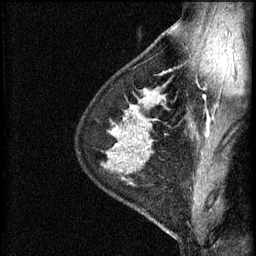
Breast MRI (dynamic contrast-enhanced), one sagittal slice. Slice 44 of 60 in the series (ordered by position). 3 images stored at this slice position (order not interpretable as contrast timing). 1.5 T. TE 4.2 ms, TR 11 ms. 2 mm slice thickness. 256 × 256 image matrix. Female patient, age 29 years.
Outlined on this slice (semi-automatically segmented with operator editing):
- analysis volume of interest (the breast-tissue region the enhancement analysis was run in; not a lesion): box from (x=106, y=172) to (x=169, y=227) px
- tumour enhancement mask (voxels above the 70 % enhancement threshold inside the analysis volume of interest): (x=131, y=172)–(x=133, y=181)